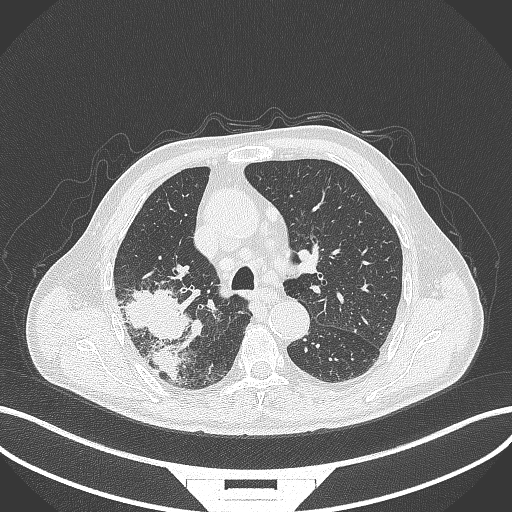
Chest CT, one axial slice; position 280 of 429 along the scan axis; reconstruction kernel B70f; lung window (W 1500 / L -600 HU); 512 × 512 image matrix, field of view 400 × 400 mm. Patient: male, 72 years. From the clinical record (not read from this slice): clinical TNM (as recorded): T3 N2 M0.
Outlined on this slice (rectangle marked by the reading radiologist):
- lung tumour (recorded histology: adenocarcinoma): box from (x=119, y=284) to (x=192, y=382) px